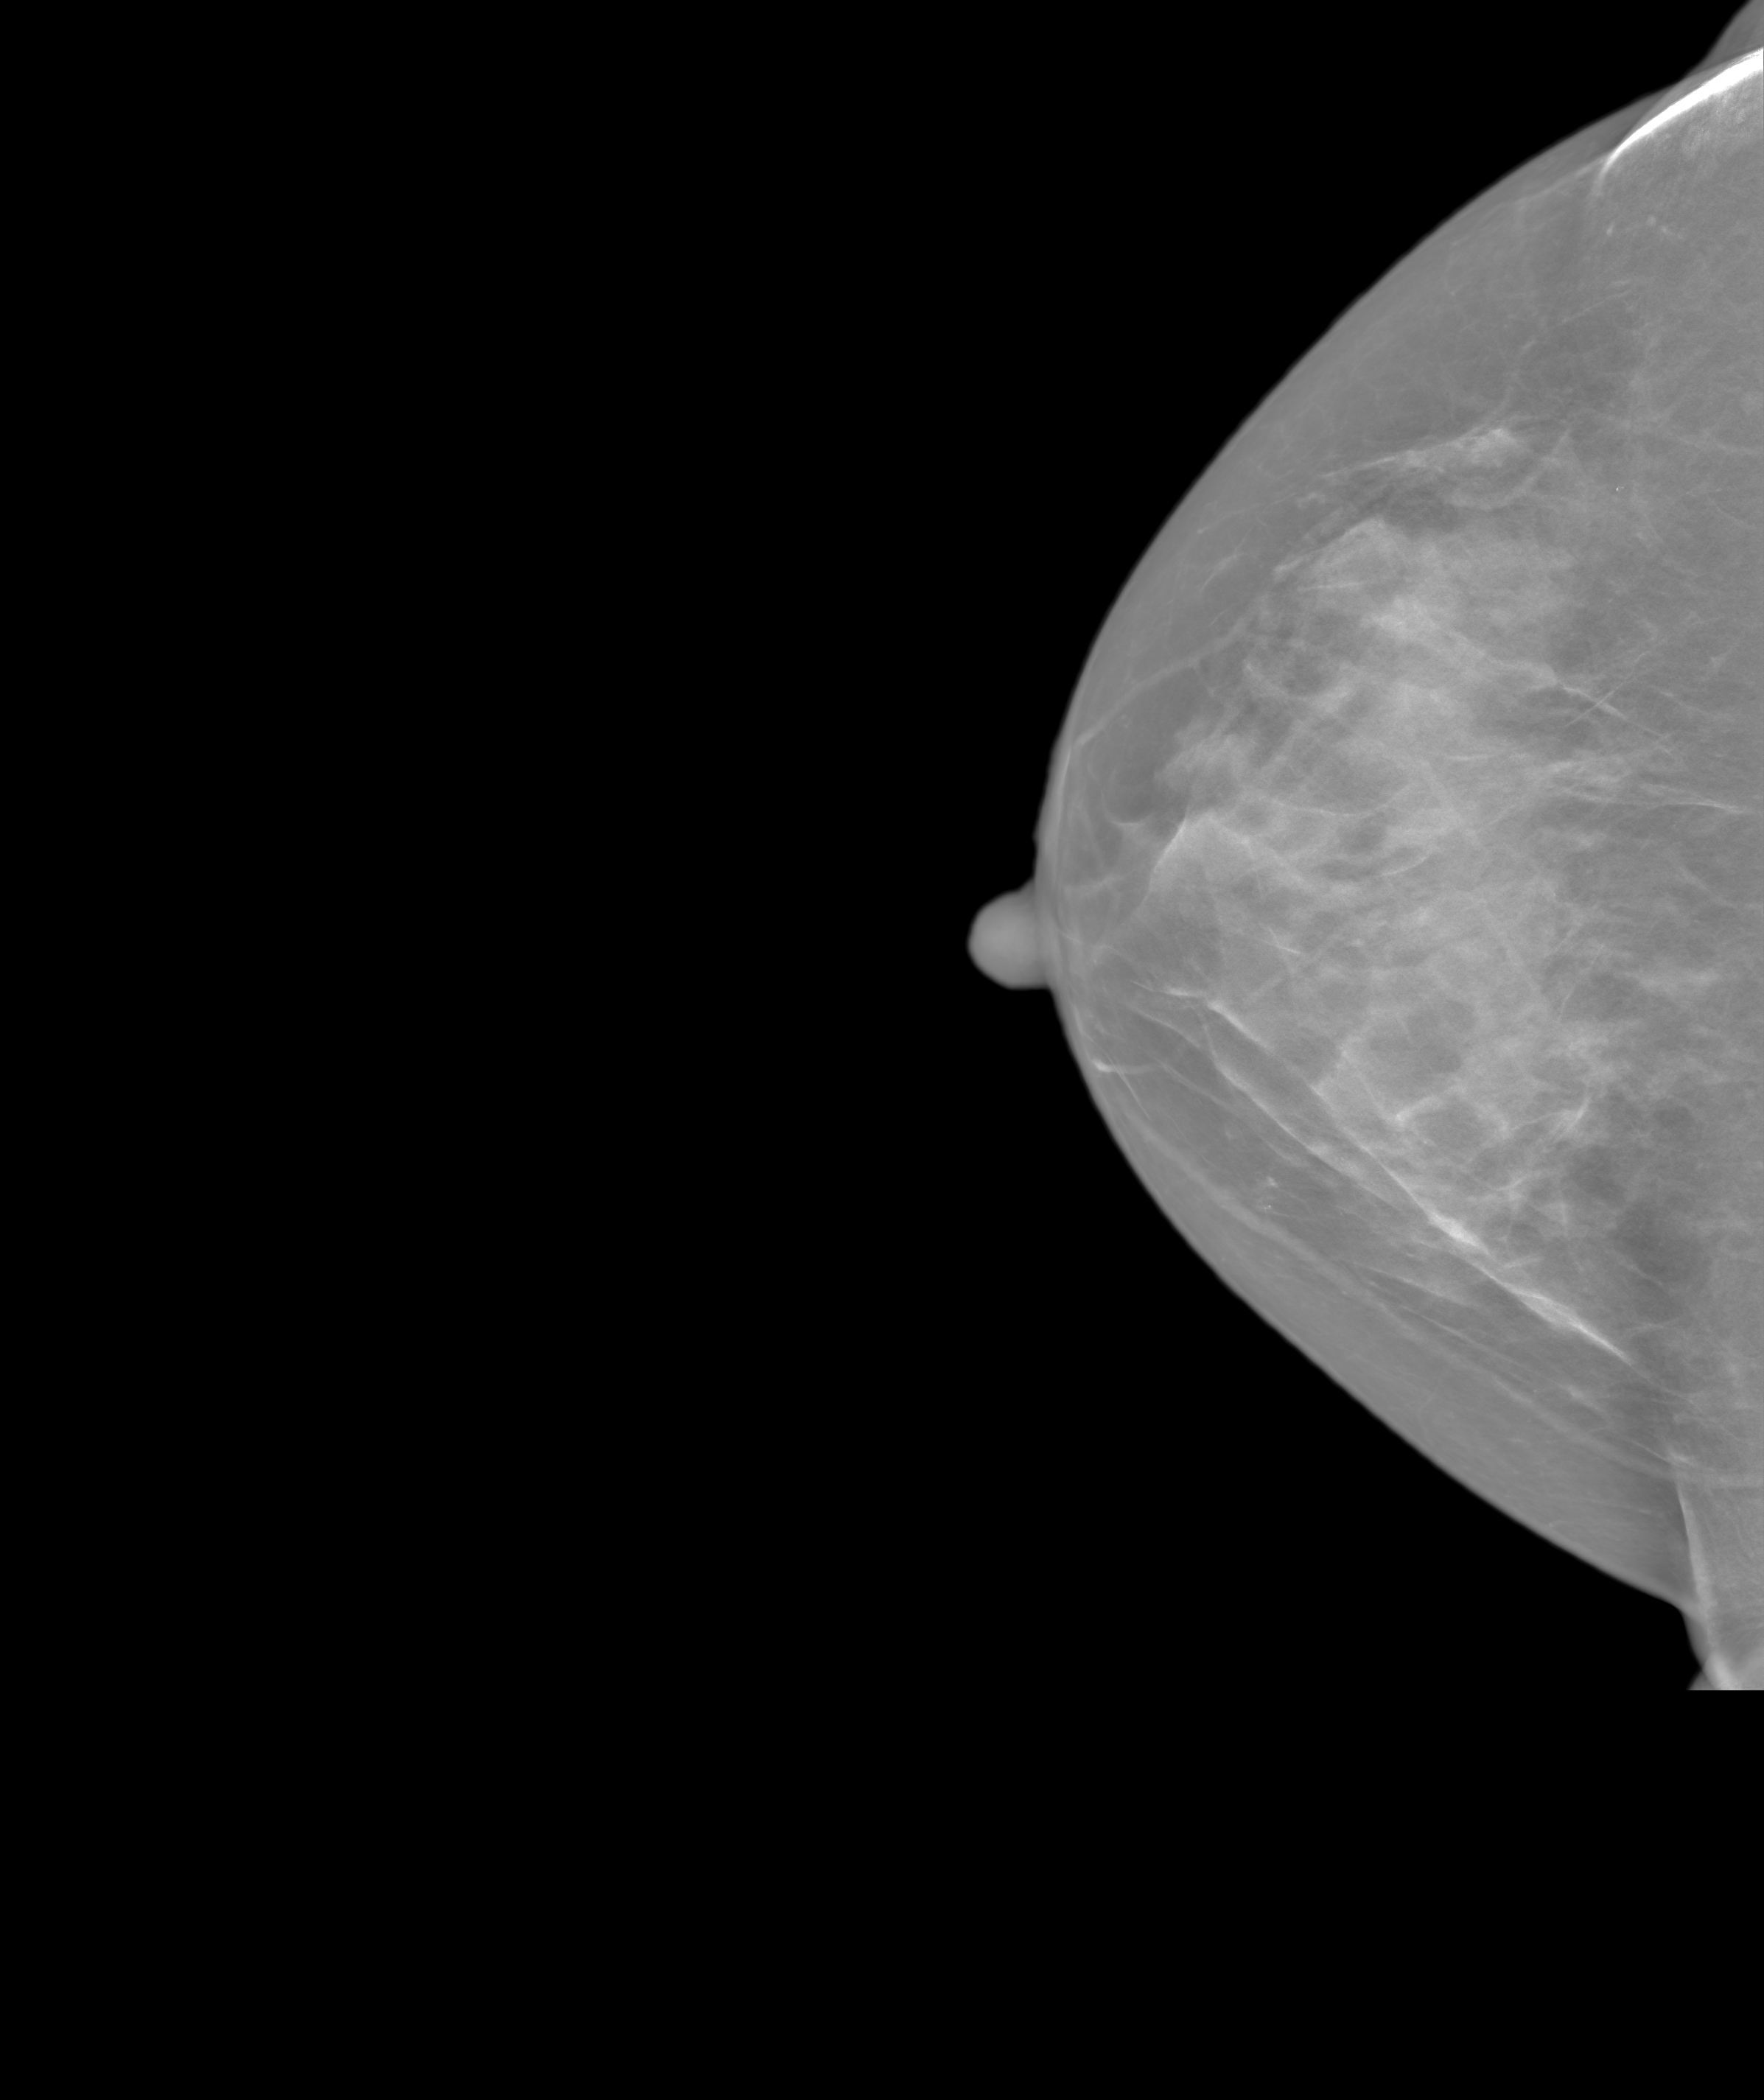
Screening examination. Female patient, age 68 years.
Image type: synthesized 2-D view from tomosynthesis. Breast: right. Projection: CC view.